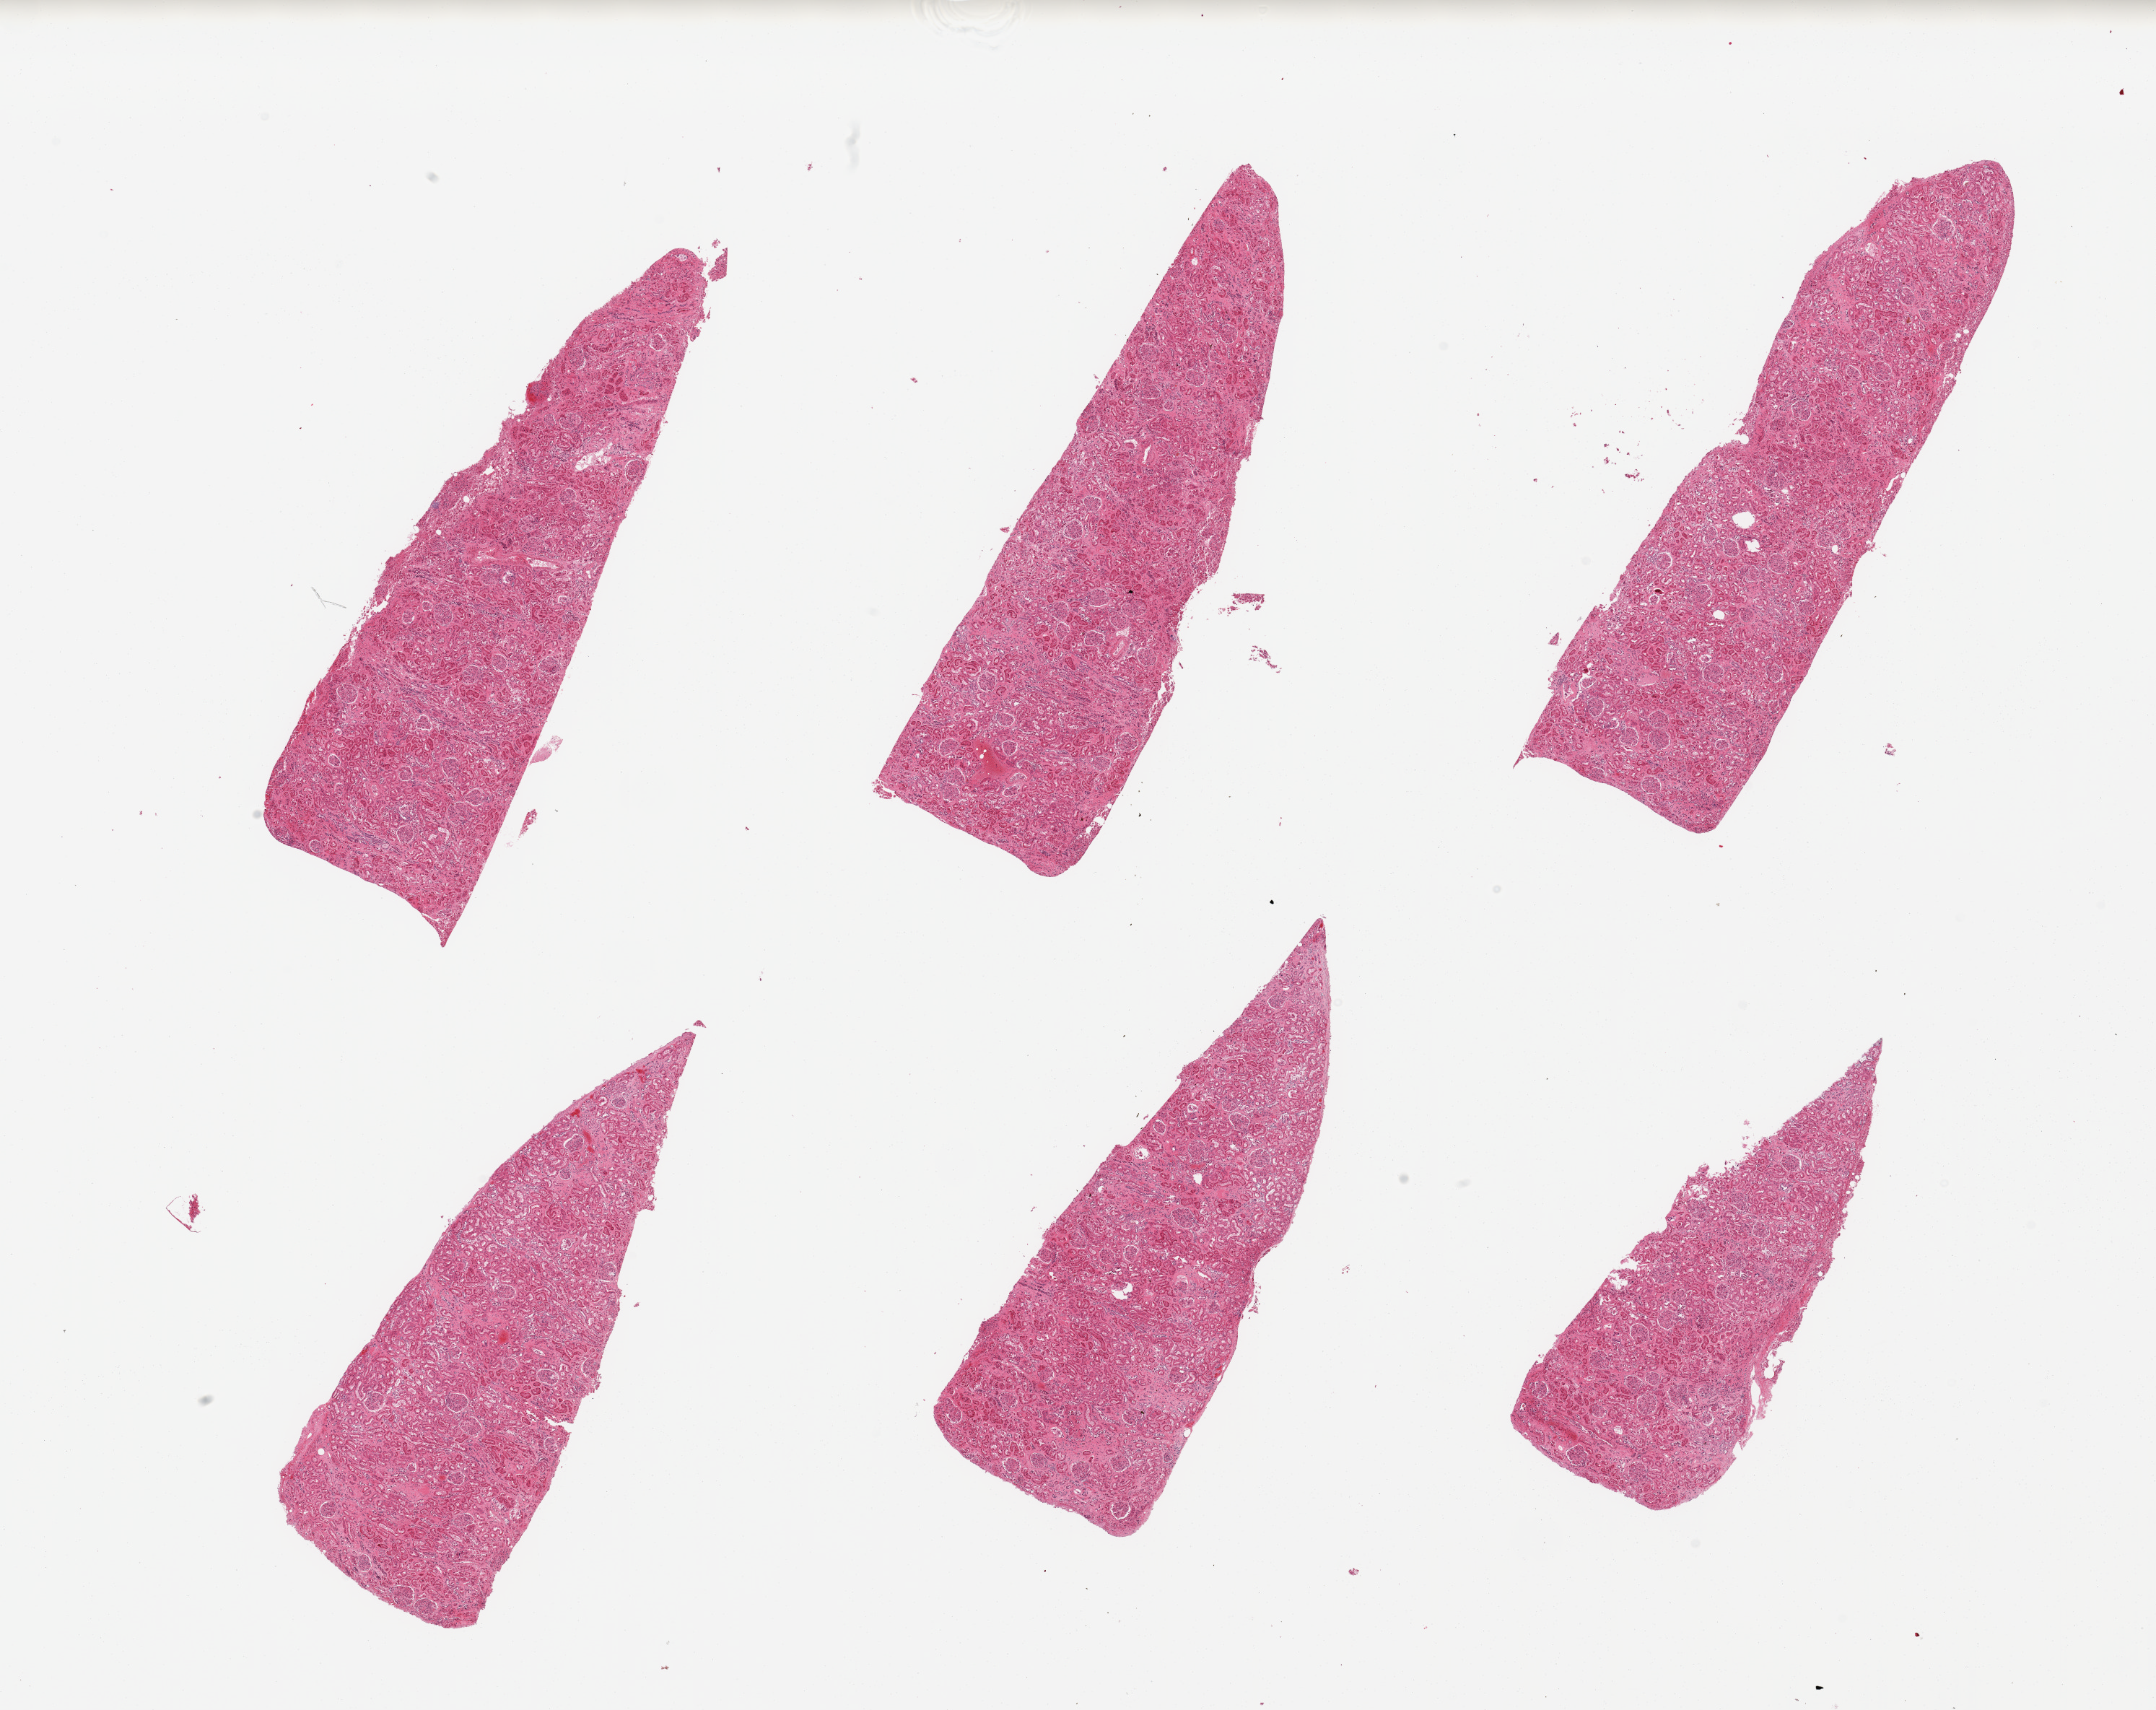
Whole-slide image, H&E stain — low-resolution overview of the scanned area, about 23.6 x 18.7 mm. PAXgene-fixed paraffin-embedded (PFPE) section. Sampled site (target tissue): renal cortex. Tissue donor sample.
Reviewer comment on this tissue sample: 6 pieces, glomeruli present; tubules variably but reasonably well preserved.